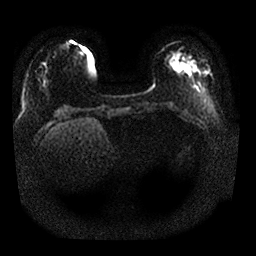
Breast MRI, one axial slice. Slice 5 of 25 in the series (ordered by position). Diffusion-weighted series; image 2 of 4 stored at this slice position (different b-values; order by instance number). 1.5 T. 4 mm slice thickness. 256 × 256 image matrix, field of view 350 × 350 mm. Female patient.
Outlined on this slice (outlined manually by an expert reader):
- tumour on diffusion-weighted imaging: box from (x=169, y=49) to (x=185, y=72) px